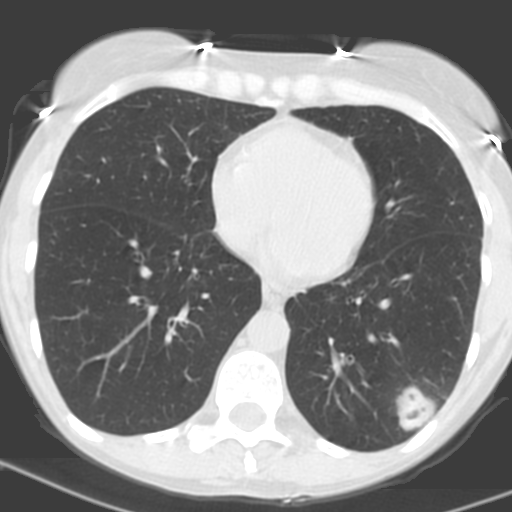
Chest CT (low-dose screening protocol), one axial image. Baseline screening round. Lung window (W 1500 / L -600 HU). 3.2 mm slice thickness. Standard (soft-tissue) reconstruction kernel (C). Slice 97 of 156 in the series. 512 × 512 image matrix. Female participant, aged 56 years at enrolment.
- Lesion marked by an expert reader, bounding box [x1, y1, x2, y2] px = [370, 366, 452, 439].
- Reader record for this screening exam (exam-level; its link to the box is not recorded): non-calcified nodule or mass ≥4 mm, left lower lobe, 31 × 23 mm, poorly defined margins, soft tissue attenuation, pre-existing on the prior screen: no.
- Official screen result: positive, change unspecified: nodule(s) >= 4 mm or enlarging nodule(s), mass(es), or other non-specific abnormalities suspicious for lung cancer.
- Participant outcome: lung cancer diagnosed 27 days after this screen — squamous cell carcinoma, NOS, left lower lobe, poorly differentiated (G3), stage IB (AJCC 6th edition), 35 mm at pathology.